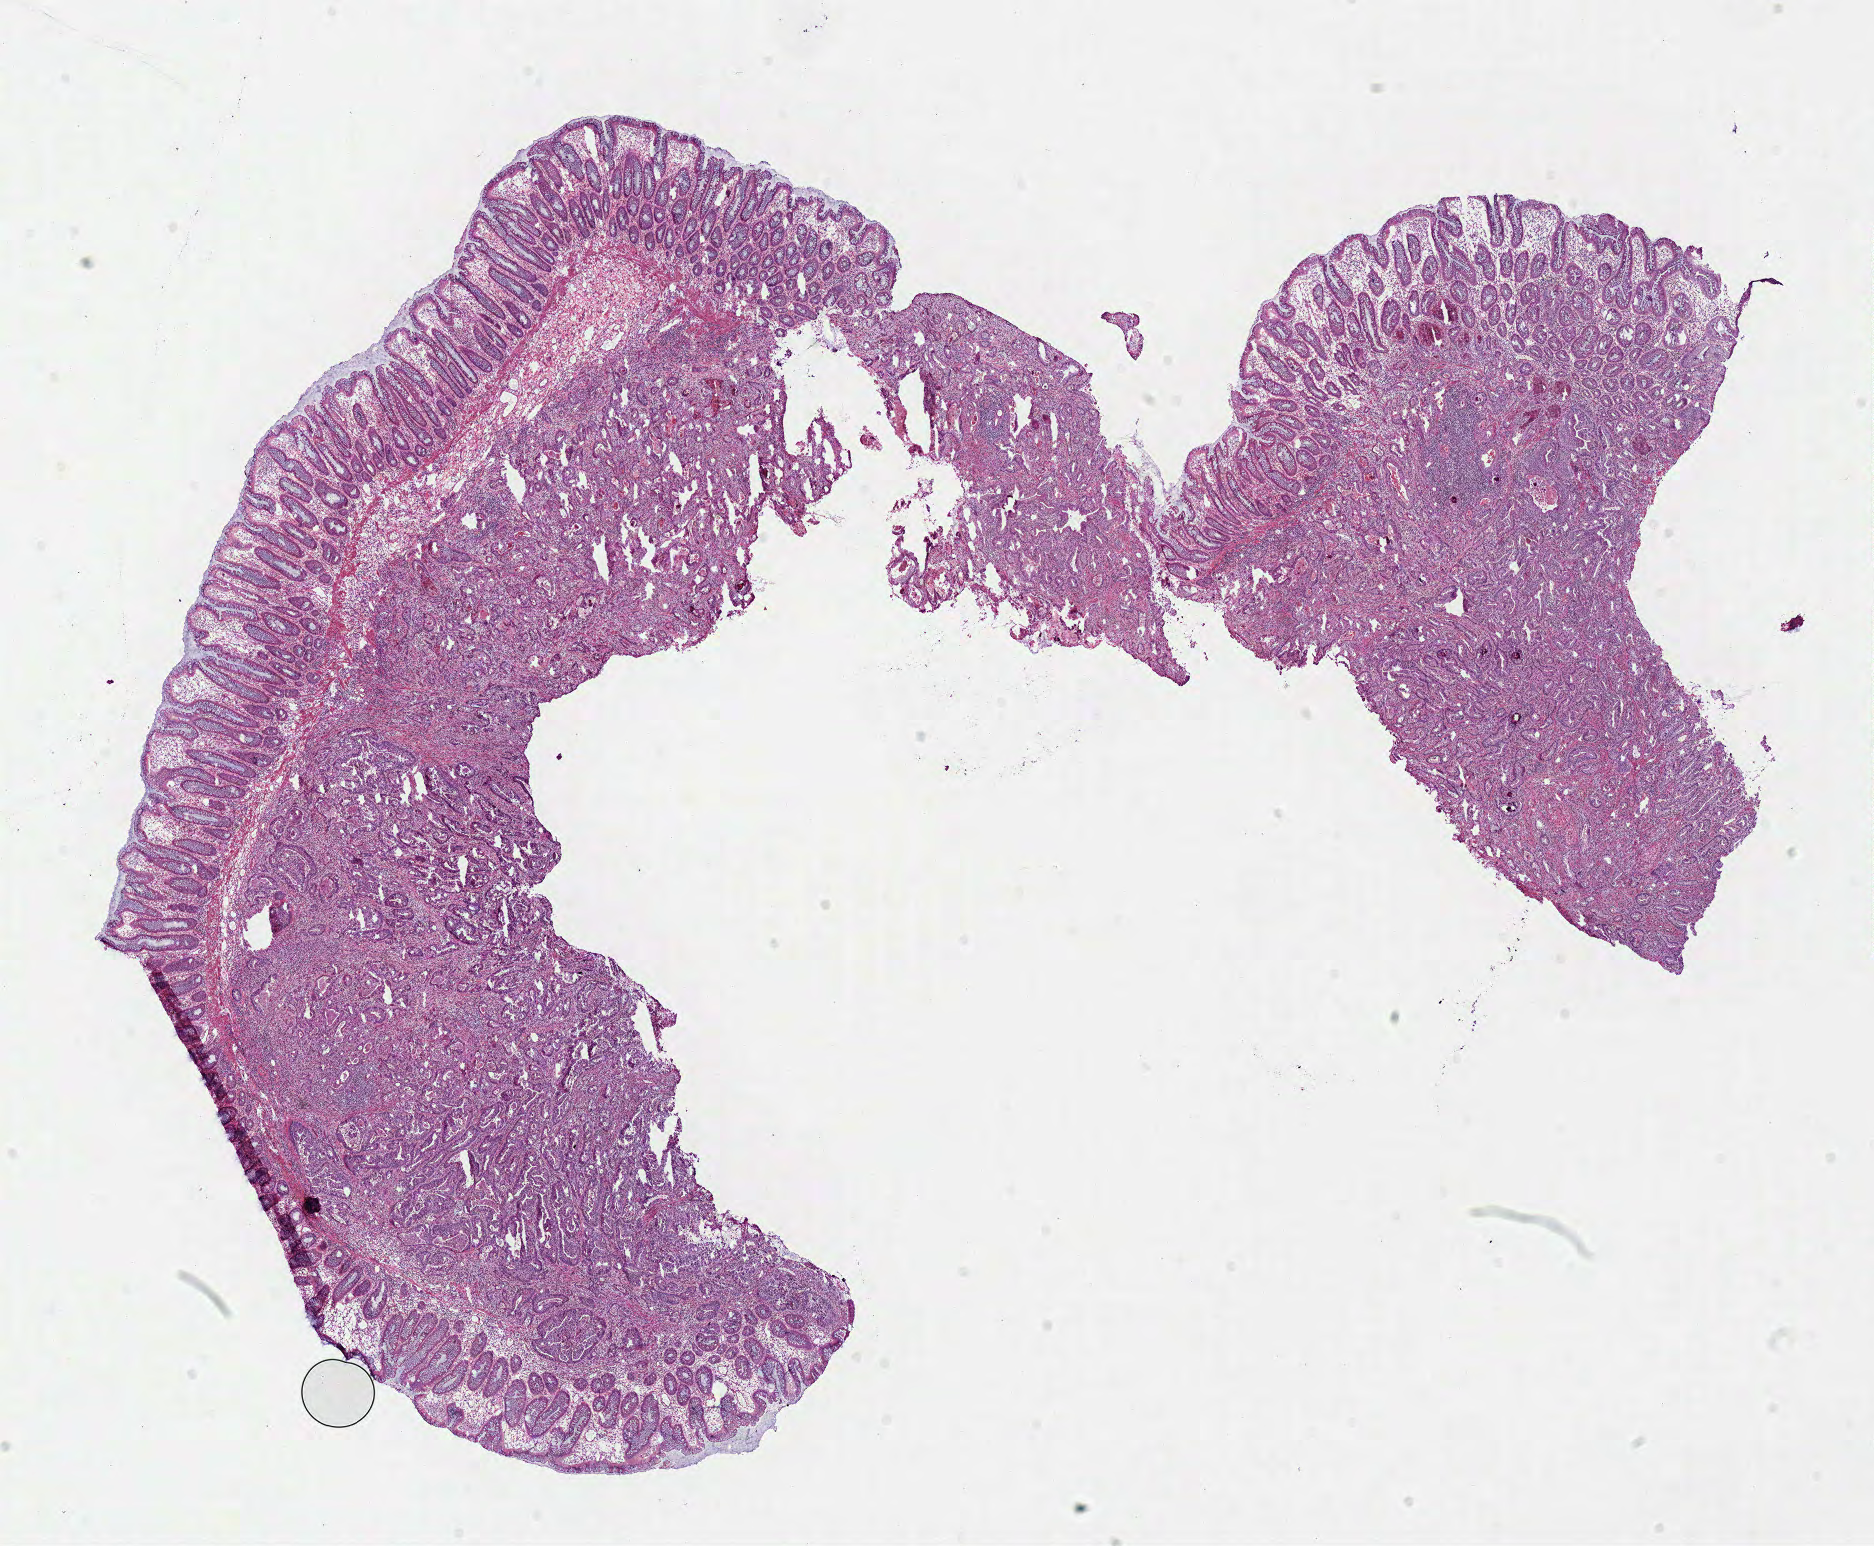
Whole-slide histology image, Hematoxylin and eosin (H&E) stained, a low-resolution overview of the entire scanned area, about 14.8 x 12.2 mm (slide scanned at 40x), frozen section from the bottom of the tissue portion, primary tumour sample from the colon. Male, age 74 years at initial diagnosis. Composition of this section per pathologist review: tumour cells 60%, tumour nuclei 60%, normal cells 20%, stromal cells 15%, necrosis 5%.
AJCC pathologic stage: I (7th edition). Pathologic diagnosis: Adenocarcinoma, NOS. Lymph nodes positive (case pathology): 0 of 23 examined.